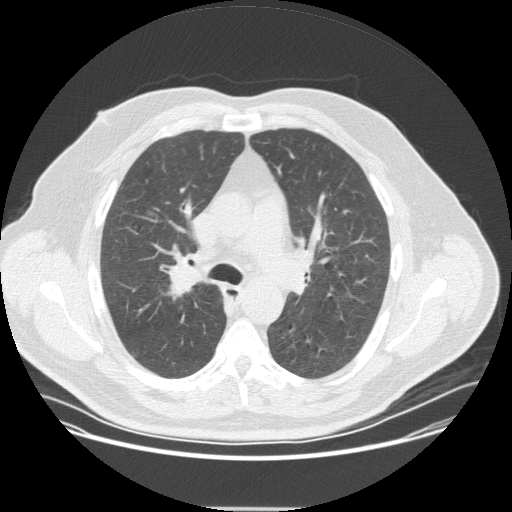
Chest CT (low-dose screening protocol), one axial image; second annual screen; lung window (W 1500 / L -600 HU); standard (soft-tissue) reconstruction kernel (STANDARD); 512 × 512 image matrix, field of view 419 × 419 mm. Male participant, aged 57 years at enrolment. Current smoker at enrolment.
- Lesion marked by an expert reader, bounding box [x1, y1, x2, y2] px = [152, 253, 211, 308].
- The exam's reader record, not a measurement of the box and not confirmed to be the same lesion: non-calcified nodule or mass ≥4 mm, right upper lobe, 20 × 16 mm, spiculated (stellate) margins, soft tissue attenuation, pre-existing on the prior screen: no.